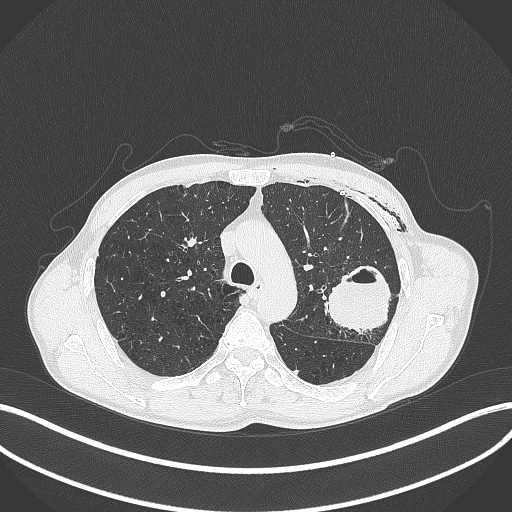
Chest CT, one axial slice. Slice 287 of 457 in the series (ordered by position). 120 kVp. Lung window (W 1500 / L -600 HU). 1 mm slice thickness. 512 × 512 image matrix. Patient: male, 58 years. Case-level facts recorded for this patient, not image findings: clinical TNM (as recorded): T3 N0 M0.
Structures marked on this image (bounding box drawn by a radiologist):
- lung tumour (recorded histology: adenocarcinoma): box from (x=321, y=262) to (x=394, y=340) px